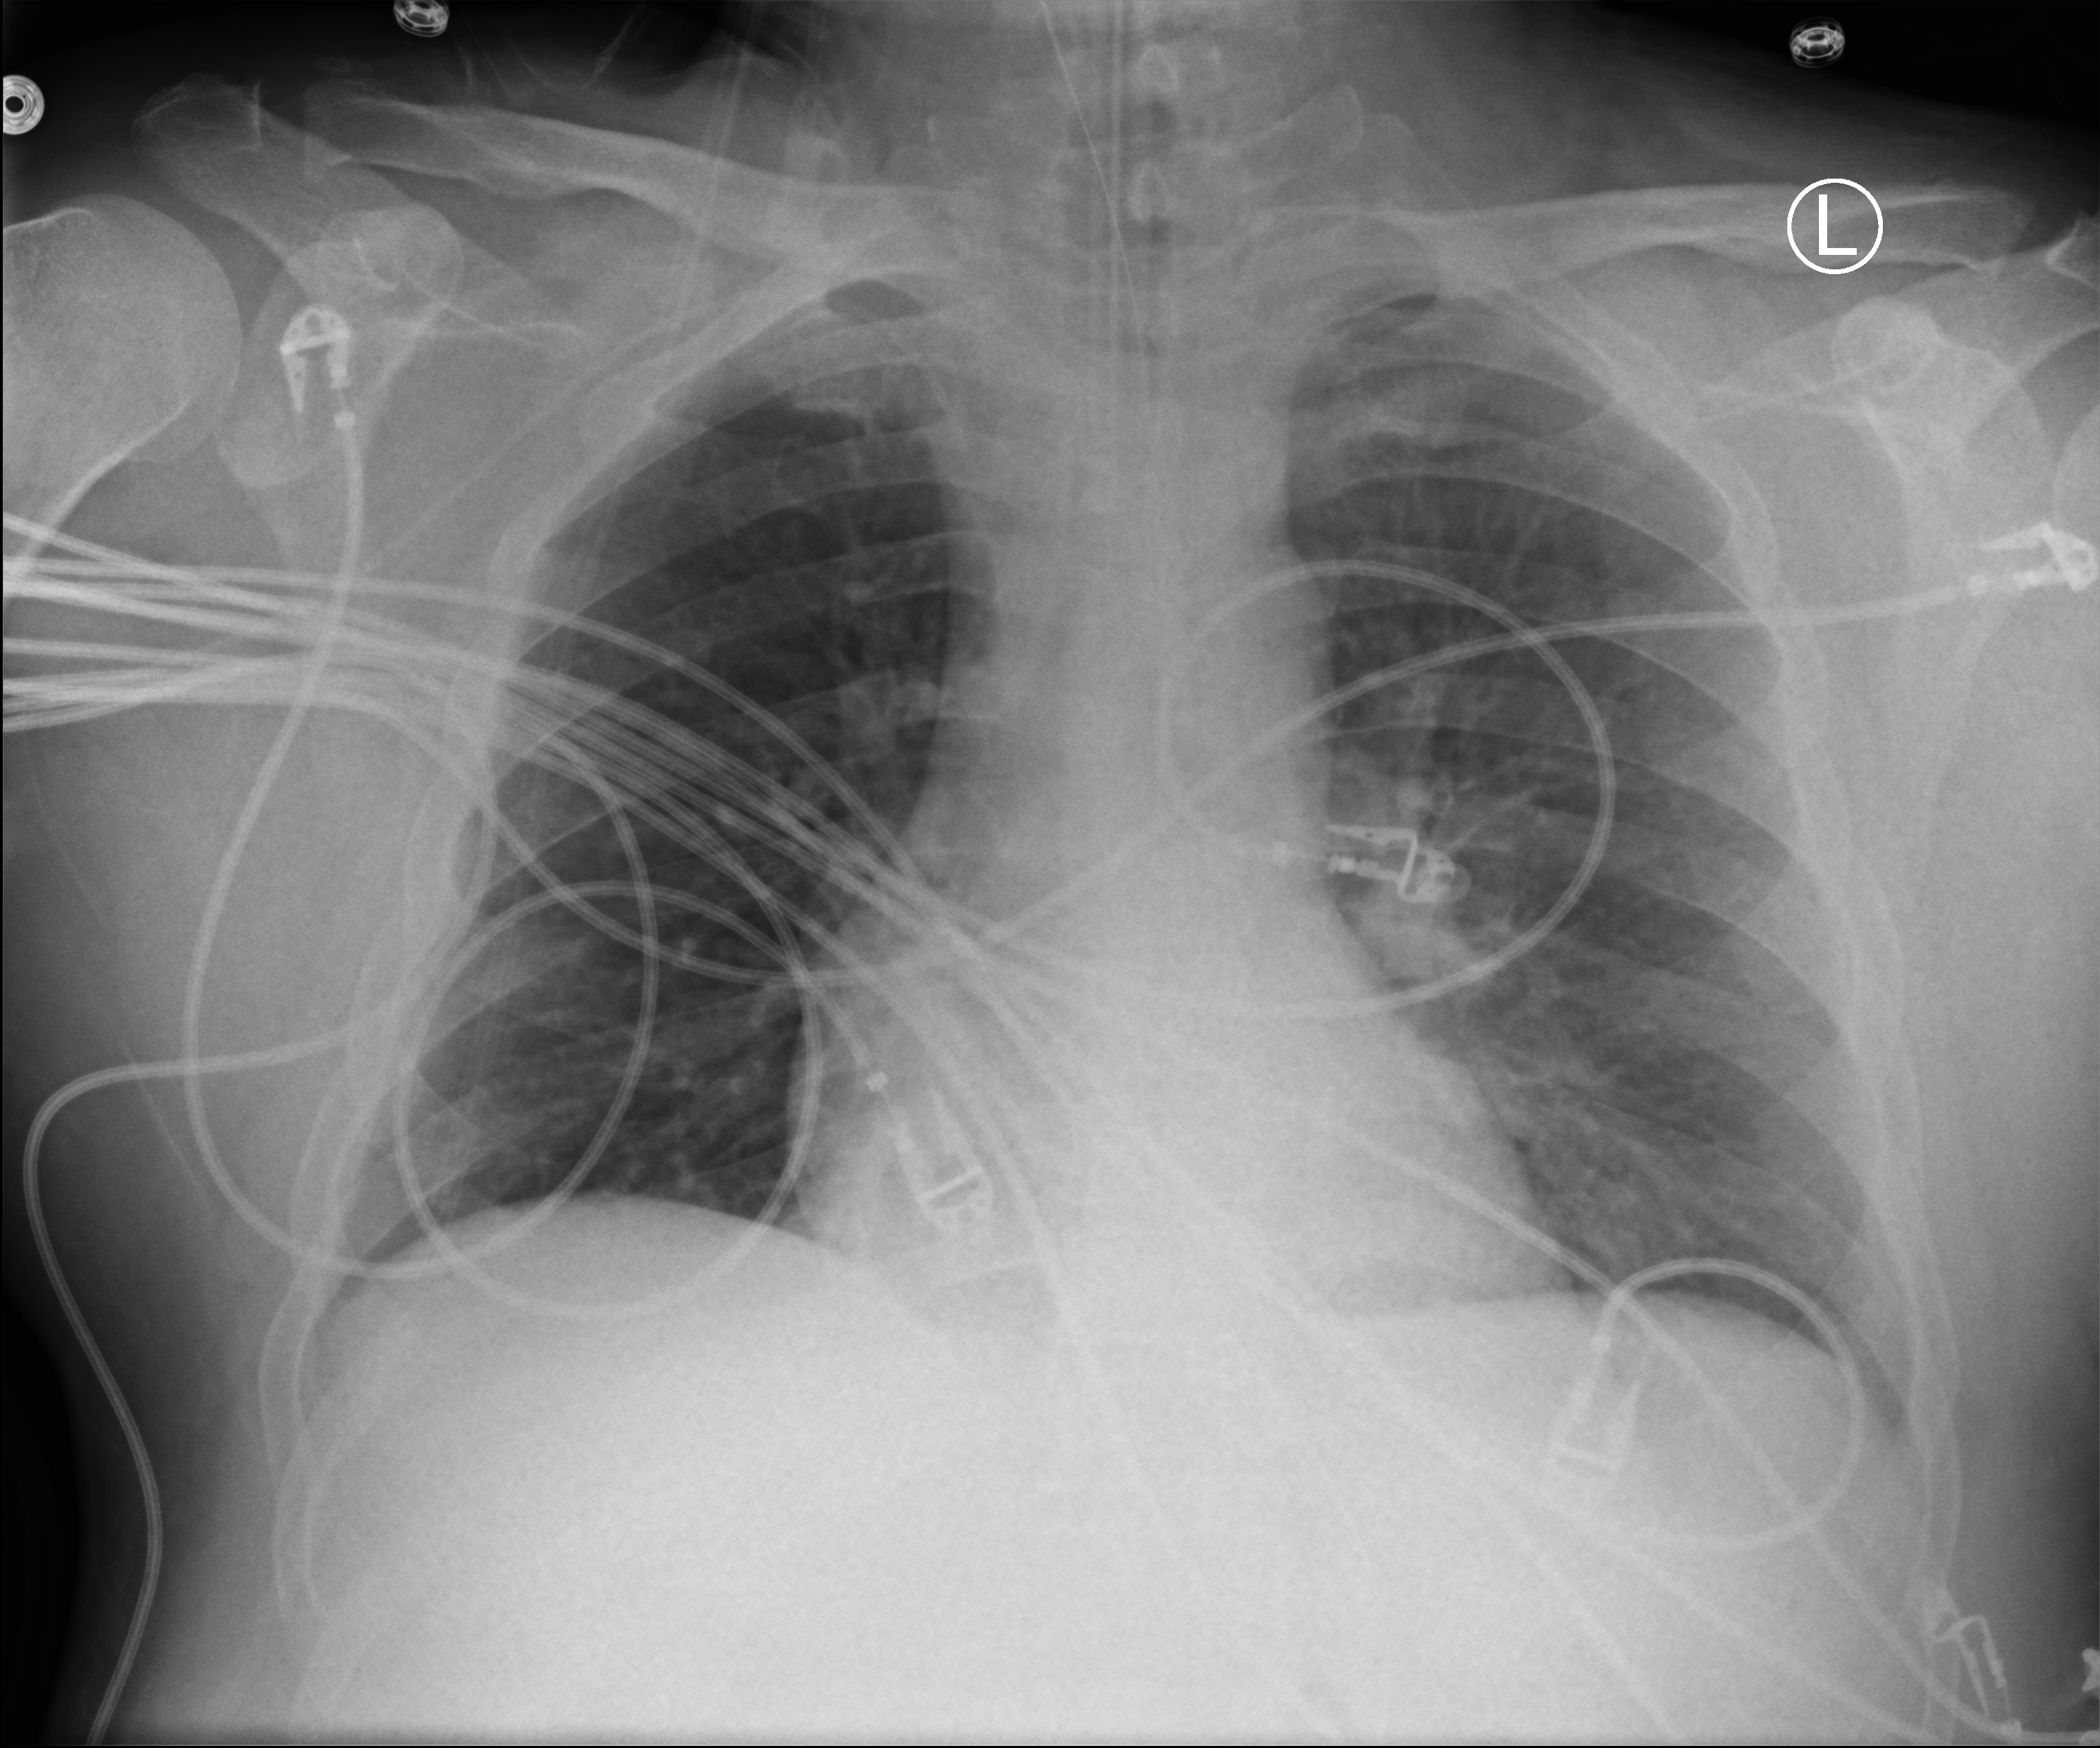
Portable chest radiograph, anteroposterior (AP) projection. Patient hospitalised with COVID-19; male, aged 18–59 years.
From the hospital-stay record, not from the radiograph (when in the stay this image was taken is not recorded): admitted to intensive care during this hospital stay: yes.